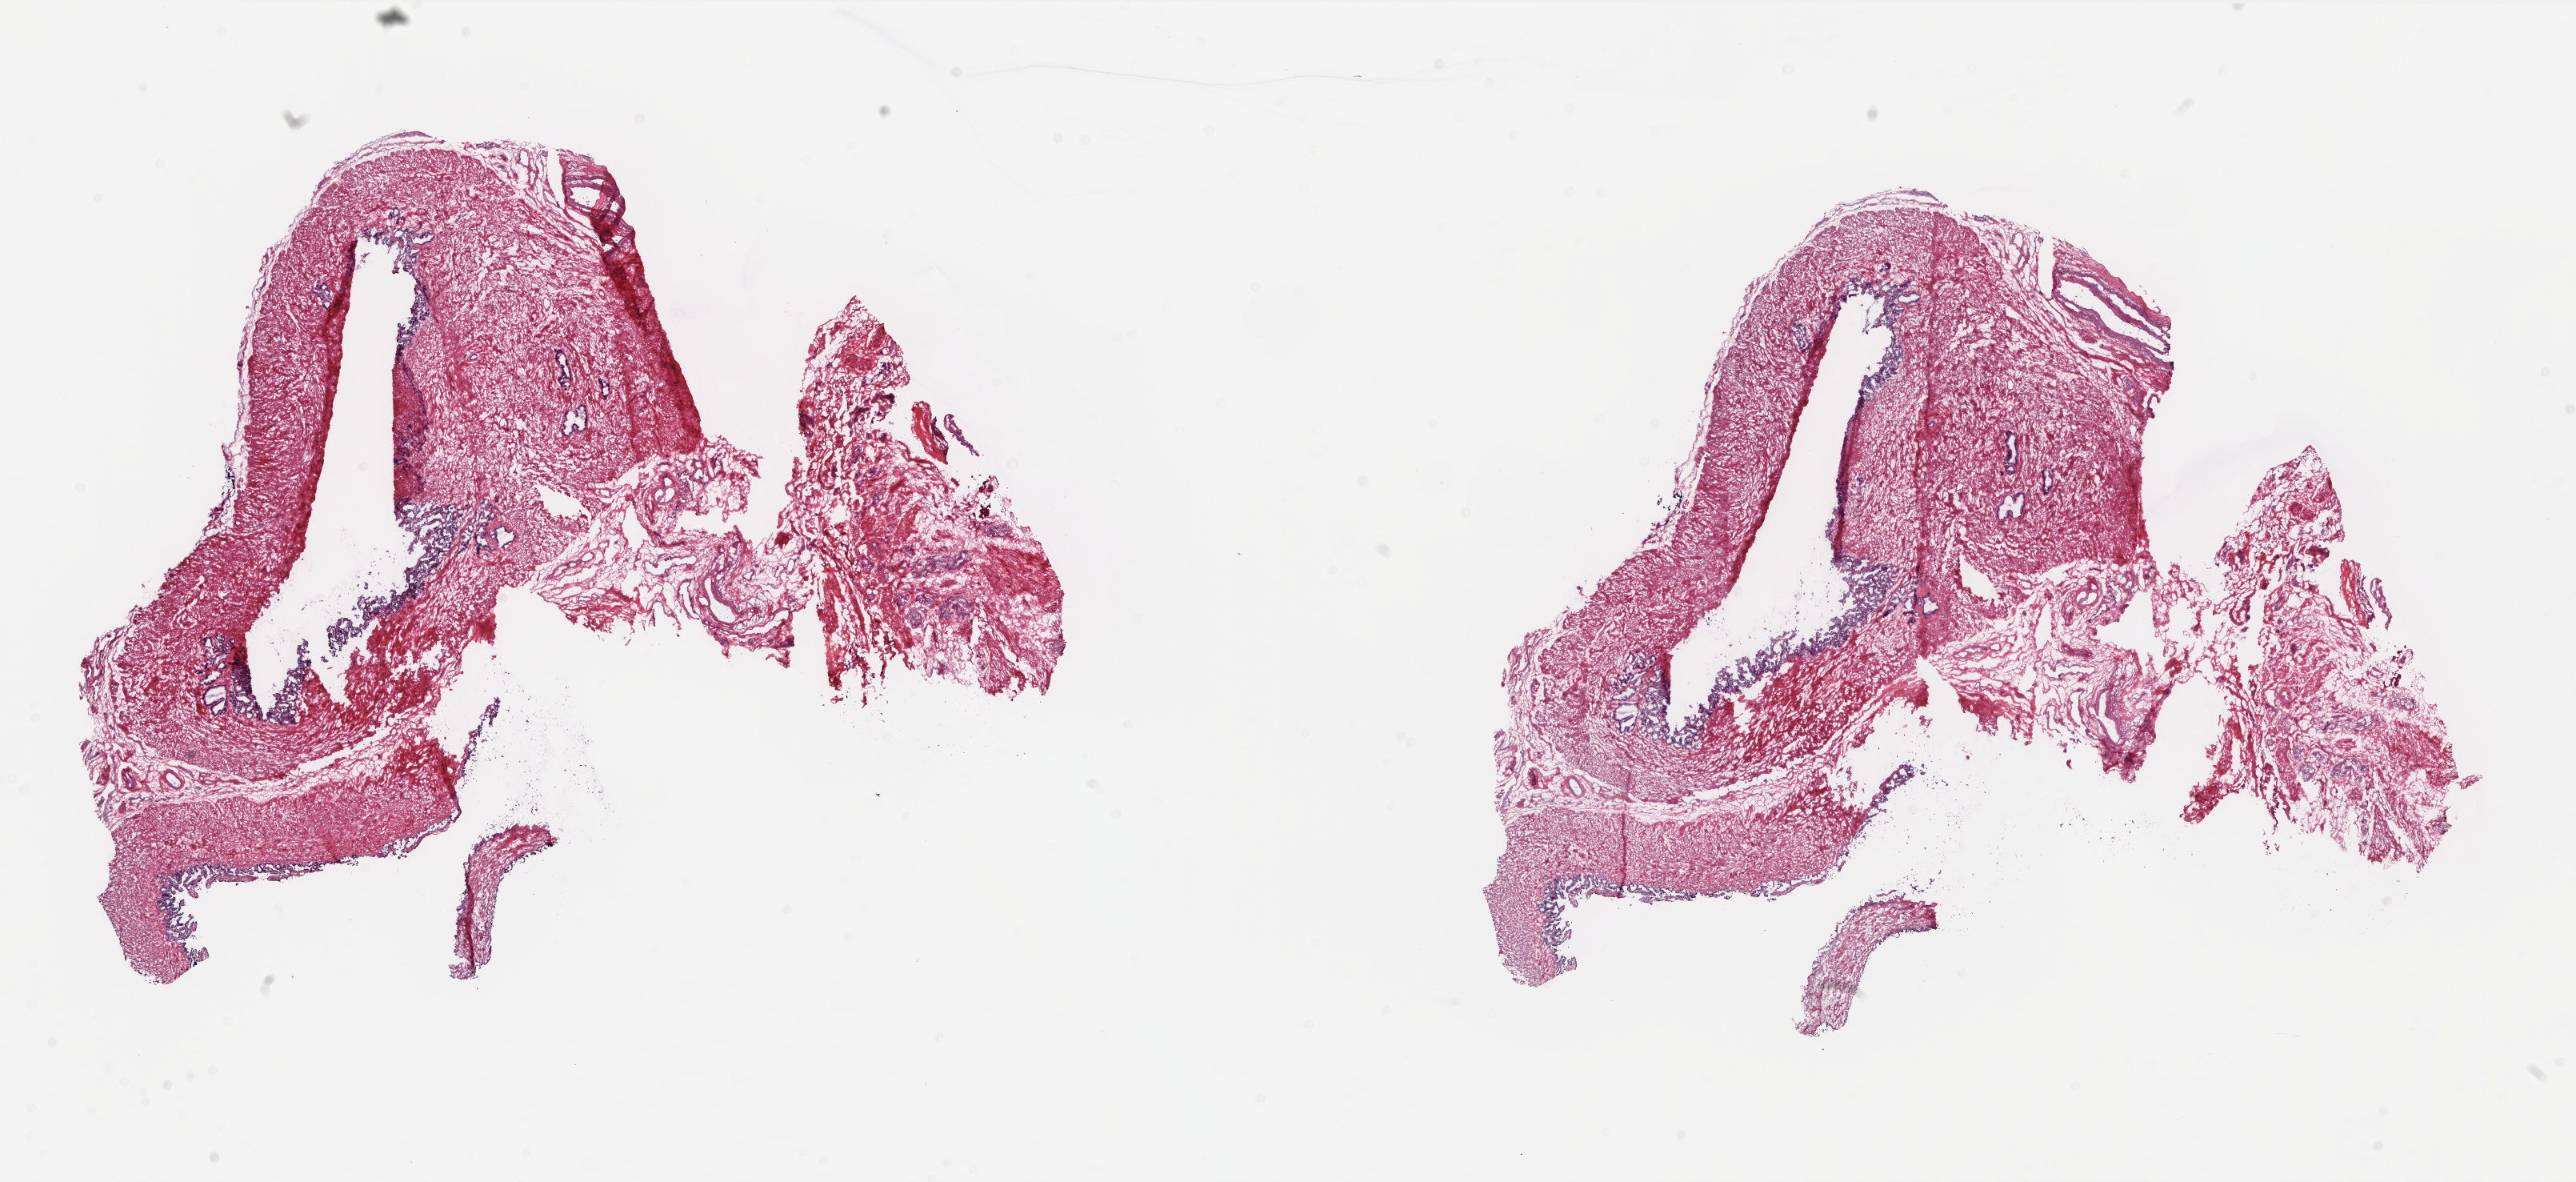
Digitized Hematoxylin and eosin (H&E) stained tissue section (whole slide) — a low-resolution overview of the entire scanned area, about 26.0 x 11.9 mm, frozen section from the top of the tissue portion, sample: solid tissue normal (non-tumour tissue), prostate. Male patient; age at initial diagnosis 69 years. Slide review estimates, as recorded: tumour cells 0%, tumour nuclei 0%, normal cells 5%, stromal cells 95%, necrosis 0%. Inflammatory infiltration, as recorded: lymphocyte infiltration 2%, monocyte infiltration 0%, neutrophil infiltration 0%.
This section: solid tissue normal sample (biorepository sample class). Patient diagnosis: Adenocarcinoma, NOS.